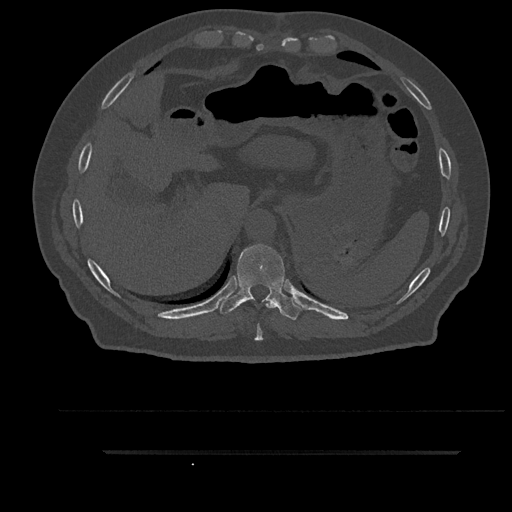
CT including the spine, one axial slice; position 384 of 797 along the scan axis; bone window (W 1800 / L 400 HU); 0.5 mm slice thickness; 512 × 512 image matrix. Male patient, age 63 years. Case-level facts recorded for this patient, not image findings: primary cancer: renal; vertebrae with lytic lesions (as recorded): T8.
Annotated regions visible in this slice (semi-automatically segmented with operator editing):
- T10 vertebra: box from (x=219, y=244) to (x=303, y=320) px
- T9 vertebra: (x=255, y=299)–(x=276, y=341)